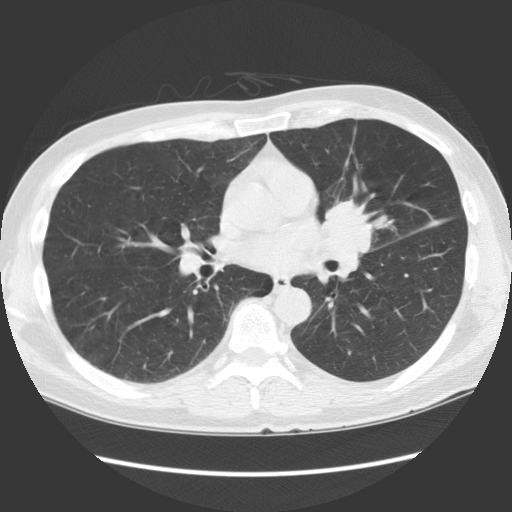
Low-dose screening chest CT, one axial slice; slice 69 of 136 in the series (ordered by position); 140 kVp; lung window (W 1500 / L -600 HU); 512 × 512 image matrix, field of view 360 × 360 mm.
Annotated regions visible in this slice (manually delineated by an expert):
- lesion 1 (tumor, hilum of left lung): bounding box (x1, y1, x2, y2) in pixels: (321, 200, 374, 255)